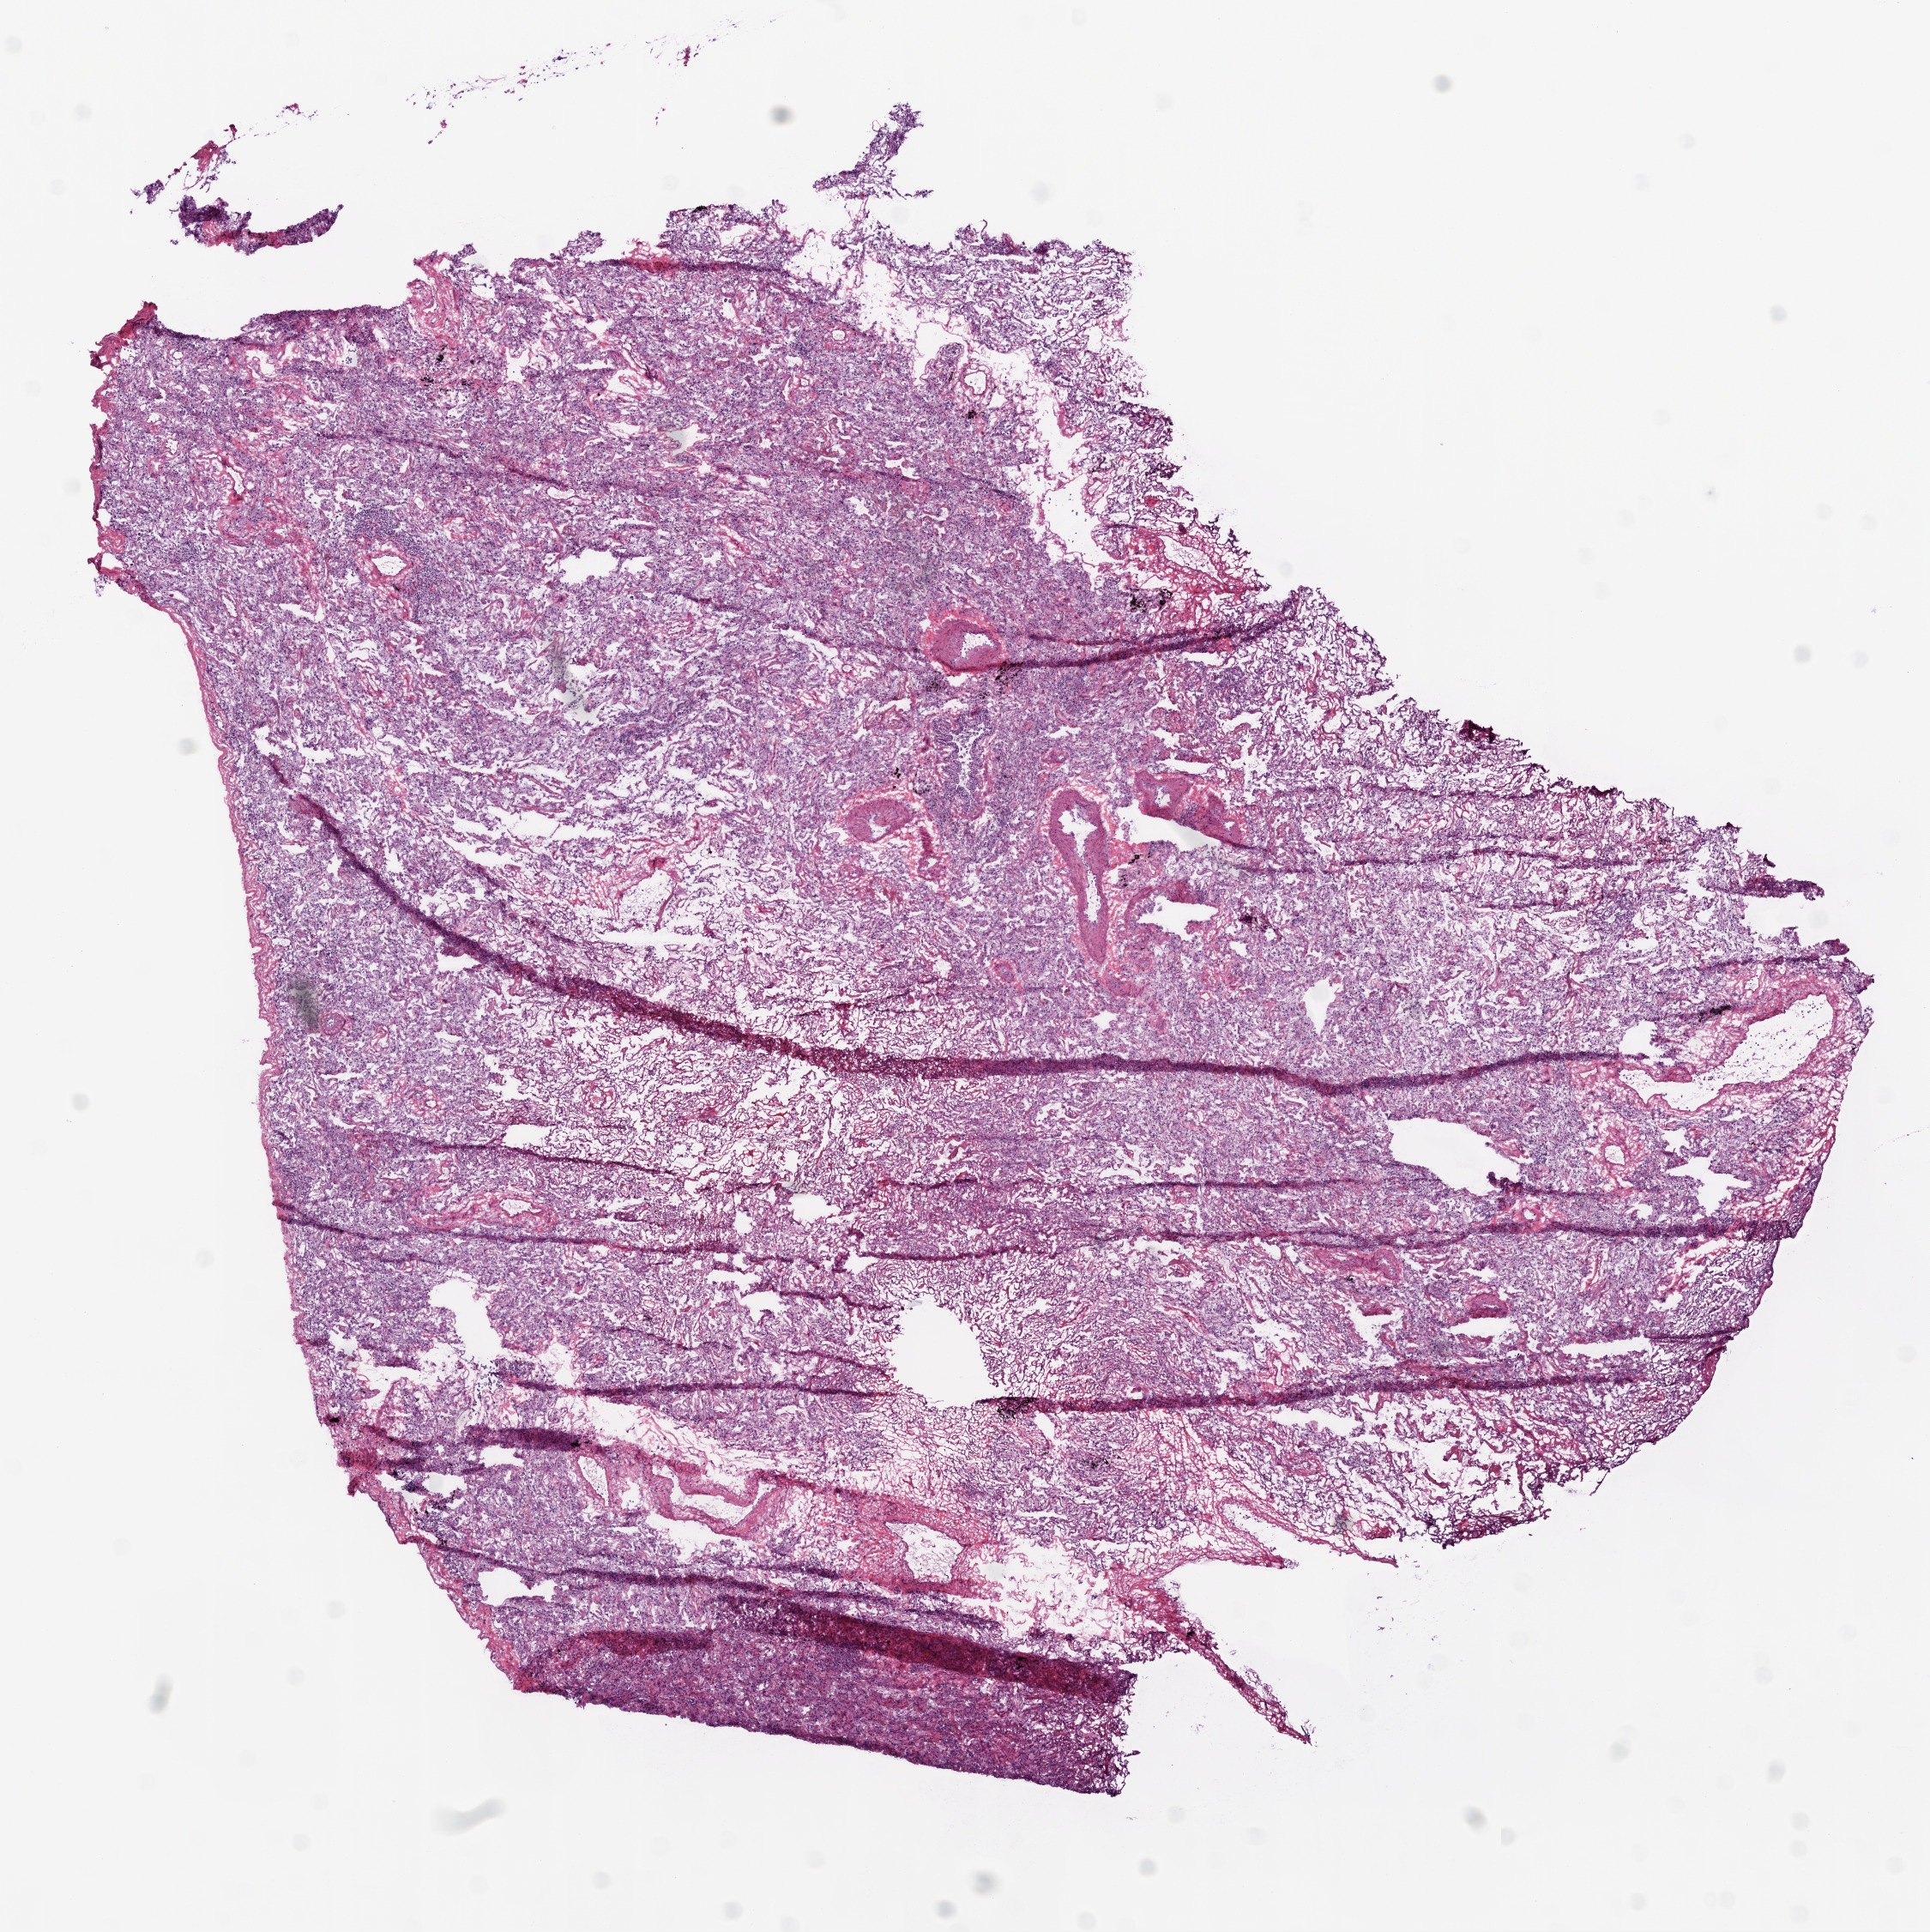
Digitized H&E tissue section (whole slide) — shown as a low-resolution overview of the whole scanned area (about 9.0 x 9.0 mm, acquisition: 20x scan); frozen section from the bottom of the tissue portion; lung, solid tissue normal (non-tumour tissue) sample. Male patient; age at initial diagnosis 70 years.
This section: solid tissue normal sample (biorepository sample class). Patient diagnosis: Squamous cell carcinoma, NOS (upper lobe, lung).